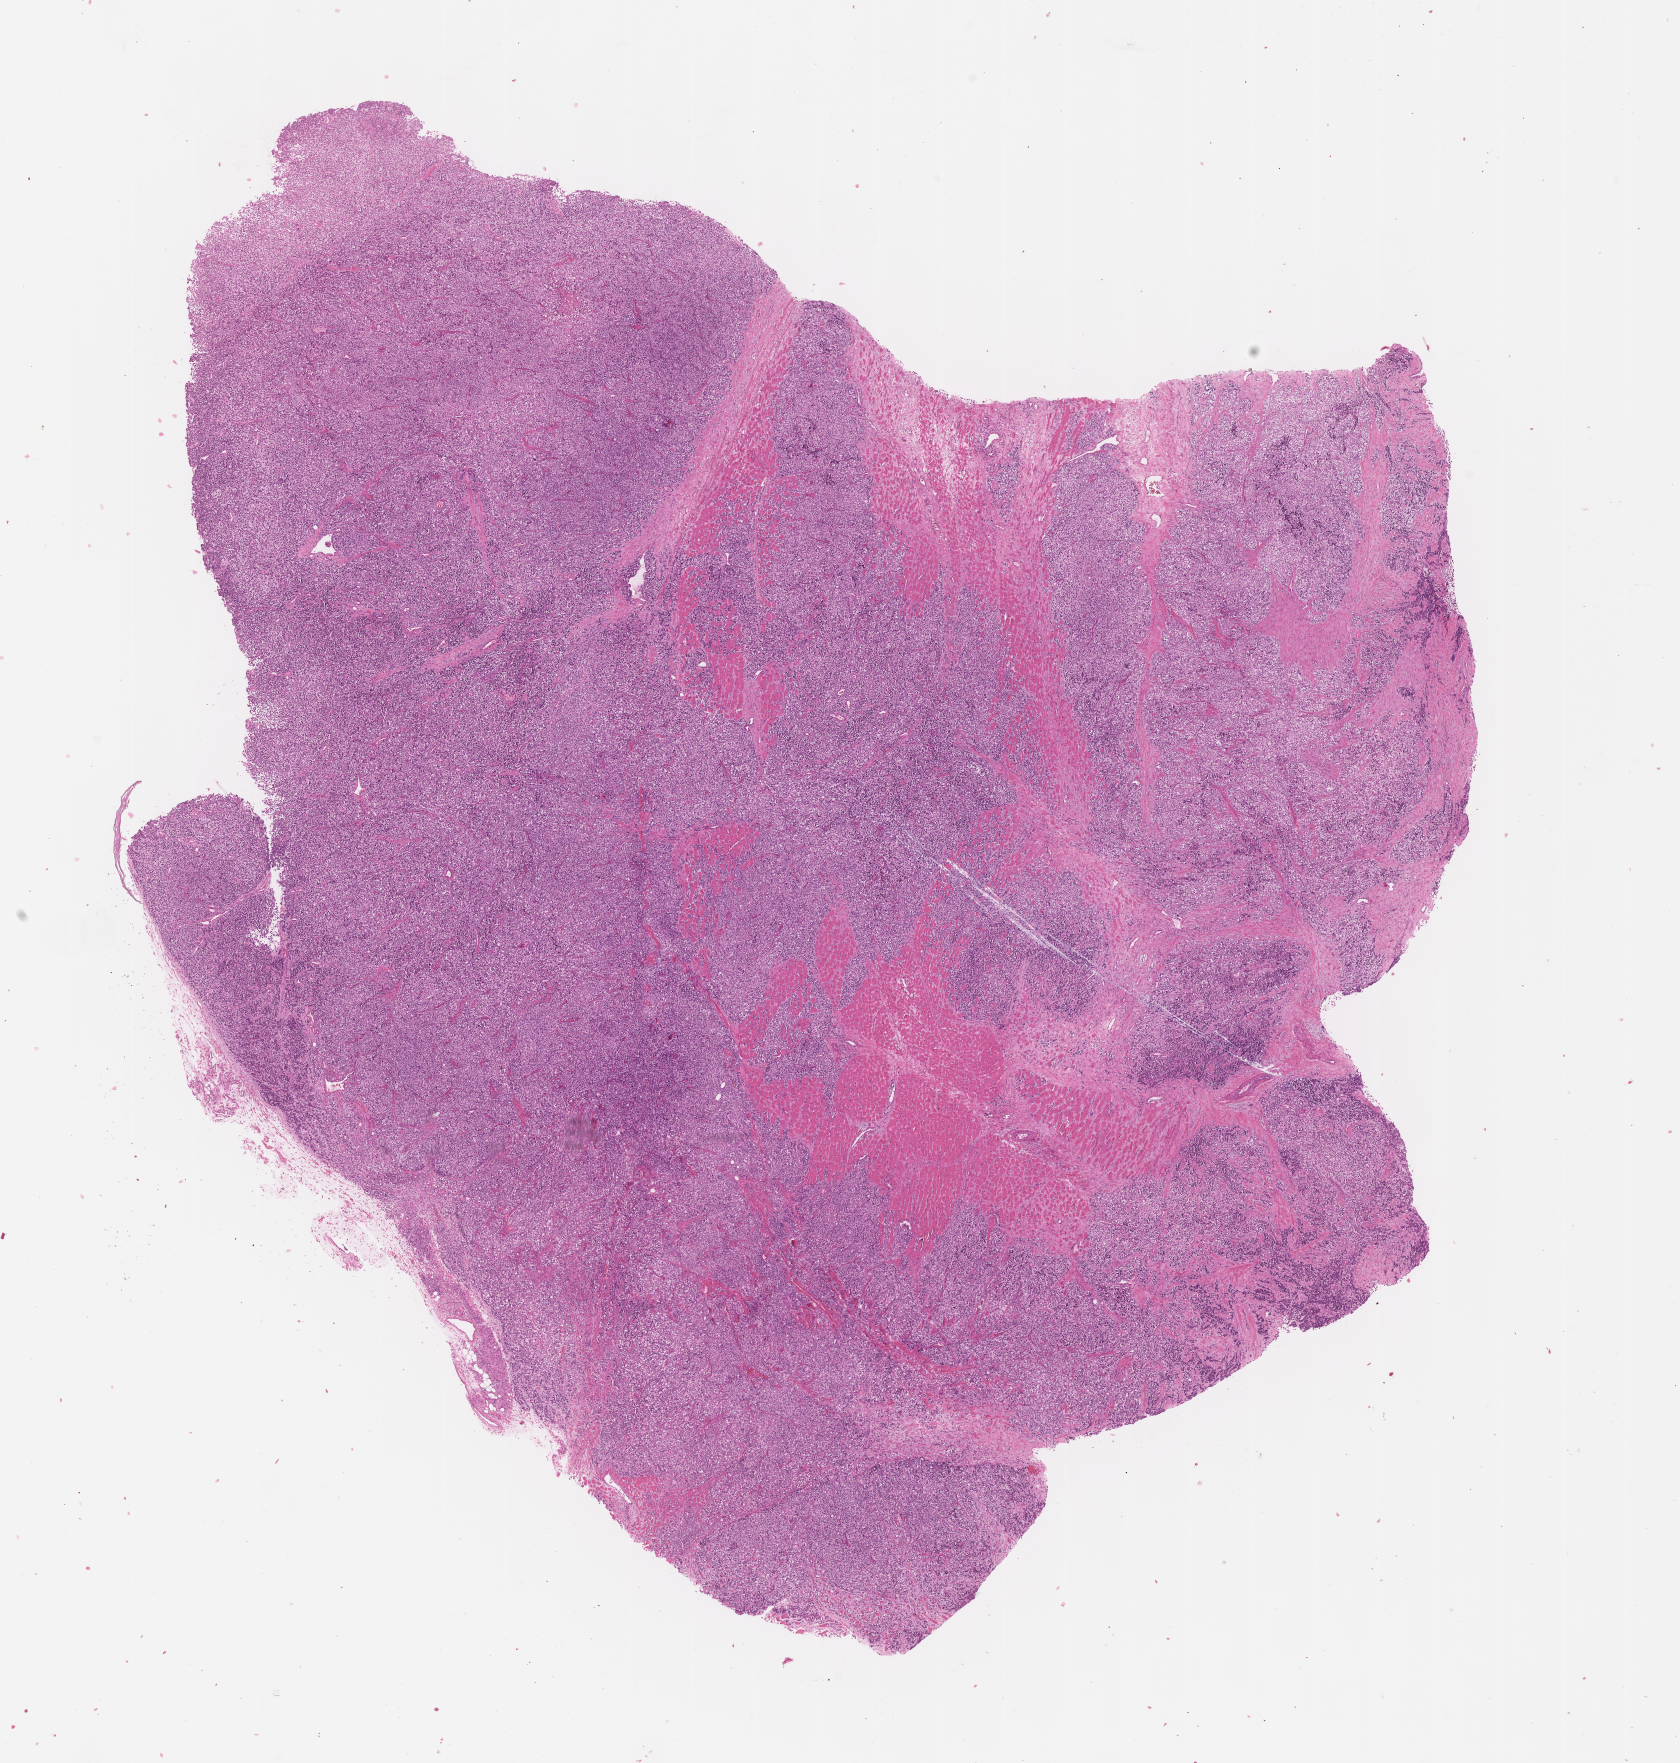
Whole-slide image, hematoxylin and eosin (H&E) stain of tumor tissue, whole scanned area (about 13.6 x 14.3 mm) shown as a low-resolution overview. Formalin-fixed paraffin-embedded section. Sample anatomic site: soft tissue, thigh-left. Male patient, age at diagnosis 3.4 years.
Stage (as recorded): 4. Metastatic status at presentation (as recorded): metastatic (confirmed). Diagnosis: rhabdomyosarcoma; histological classification: alveolar rhabdomyosarcoma.